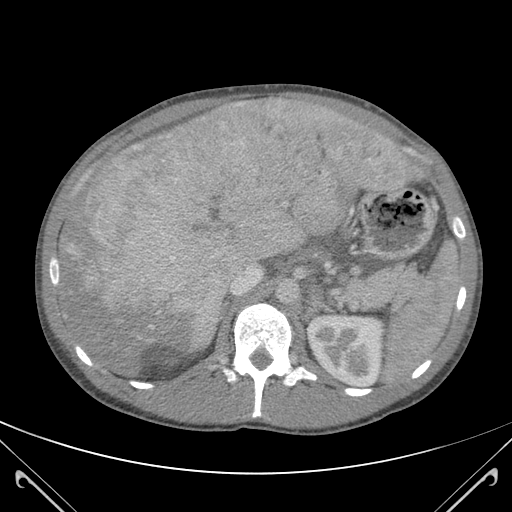
Contrast-enhanced abdominal CT (liver protocol), one axial slice; slice 74 of 118 in the series (ordered by position); 120 kVp; soft-tissue window (W 400 / L 40 HU); 3 mm slice thickness; 512 × 512 image matrix, field of view 380 × 380 mm. From the clinical record (not read from this slice): diagnosis: hepatocellular carcinoma (patient treated with transarterial chemoembolisation; whether this scan precedes or follows treatment is not stated here); TNM stage (as recorded): Stage-IIIB; Child-Pugh class: A; tumour nodularity: uninodular.
Outlined on this slice (semi-automatic segmentation, software-assisted and operator-edited):
- abdominal aorta: bounding box <276,279,298,304> (left, top, right, bottom; pixels)
- liver parenchyma outside the tumour (the mass and vessels are separate outlines, so this box may not span the whole liver): <57,99,424,379>
- mass: <64,101,418,352>
- liver vessels: <68,100,391,295>